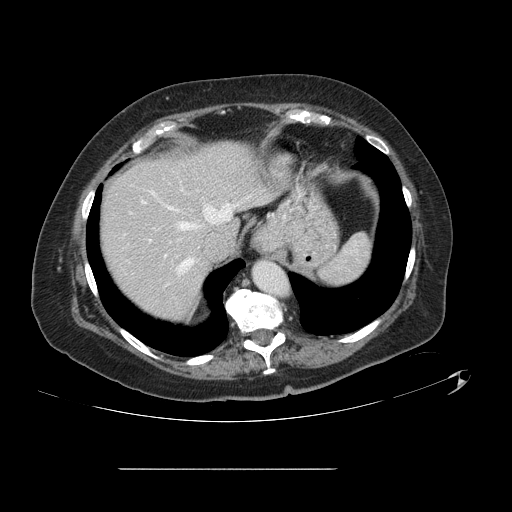
Contrast-enhanced abdominal CT, one axial slice; slice 111 of 148 in the series (ordered by position); soft-tissue window (W 400 / L 40 HU); 2.5 mm slice thickness; 512 × 512 image matrix. Female patient, age 75 years. From the clinical record (not read from this slice): diagnosis: colorectal cancer liver metastases, imaged before liver resection; multiple liver metastases: no; largest metastasis: 2.4 cm.
Structures marked on this image (outlined manually by an expert reader):
- hepatic veins: bounding box [x1, y1, x2, y2] px = [152, 193, 239, 275]
- liver: [99, 142, 267, 321]
- planned liver remnant (the part of the liver to remain after resection): [99, 141, 266, 321]
- portal vein (with intrahepatic branches): [142, 201, 151, 241]